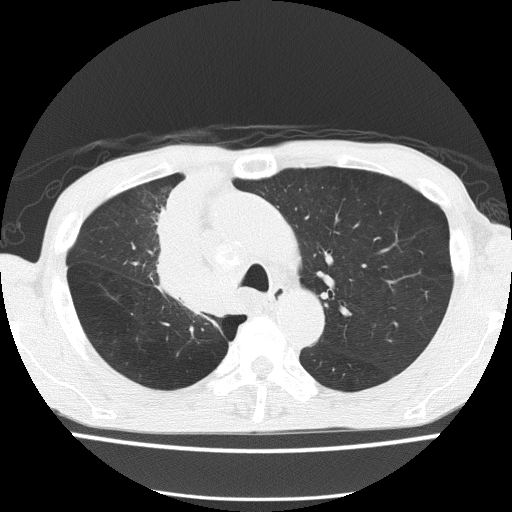
Axial slice from a low-dose chest CT screening exam, baseline annual screen, lung window (W 1500 / L -600 HU), 2 mm slice thickness, slice 46 of 150 in the series, 512 × 512 image matrix, field of view 336 × 336 mm. Male participant, aged 59 years at enrolment.
Expert-annotated lung lesion, bounding box [x1, y1, x2, y2] px = [136, 232, 235, 324]. The screening reader recorded 5 non-calcified nodules or masses ≥4 mm on this exam (left upper lobe, left upper lobe, left upper lobe, right middle lobe, right lower lobe); which of them this box marks is not recorded. Official screen result: positive, change unspecified: nodule(s) >= 4 mm or enlarging nodule(s), mass(es), or other non-specific abnormalities suspicious for lung cancer. Lung cancer was diagnosed 72 days after this screen: squamous cell carcinoma, NOS, right upper lobe, moderately differentiated (G2), stage IV (AJCC 6th edition).